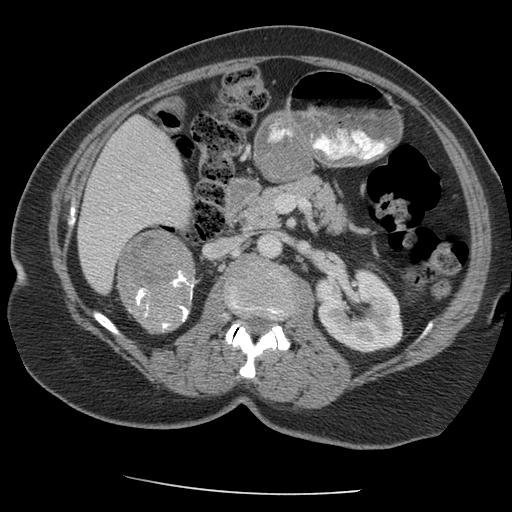
Contrast-enhanced abdominal CT, one axial slice. Slice 112 of 163 in the series (ordered by position). Reconstruction kernel STANDARD. 140 kVp. Intravenous contrast given. Soft-tissue window (W 400 / L 40 HU). 512 × 512 image matrix, field of view 360 × 360 mm. Female patient, age 70 years. Case-level facts recorded for this patient, not image findings: diagnosis: adrenocortical carcinoma; tumour side: right adrenal; tumour size at pathology: 9.5 cm; Ki-67 index: 5 %; stage (as recorded): 2.
Outlined on this slice (semi-automatic segmentation, software-assisted and operator-edited):
- mass: bounding box [x1, y1, x2, y2] px = [119, 230, 194, 333]